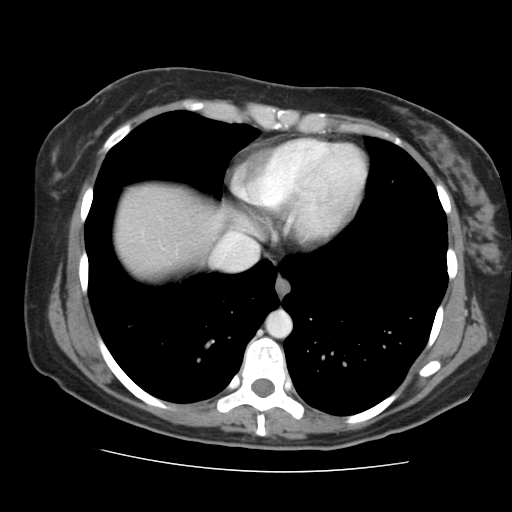
Contrast-enhanced abdominal CT, one axial slice; position 137 of 144 along the scan axis; 120 kVp; intravenous contrast given; soft-tissue window (W 400 / L 40 HU); 2.5 mm slice thickness; 512 × 512 image matrix, field of view 333 × 333 mm. Female patient, age 46 years. Case-level facts recorded for this patient, not image findings: diagnosis: colorectal cancer liver metastases, imaged before liver resection; multiple liver metastases: no; largest metastasis: 2.8 cm; disease in both lobes: no.
Structures marked on this image (outlined manually by an expert reader):
- hepatic veins: bounding box (x1, y1, x2, y2) in pixels: (214, 239, 258, 270)
- liver: (118, 184, 228, 277)
- planned liver remnant (the part of the liver to remain after resection): (118, 184, 228, 277)